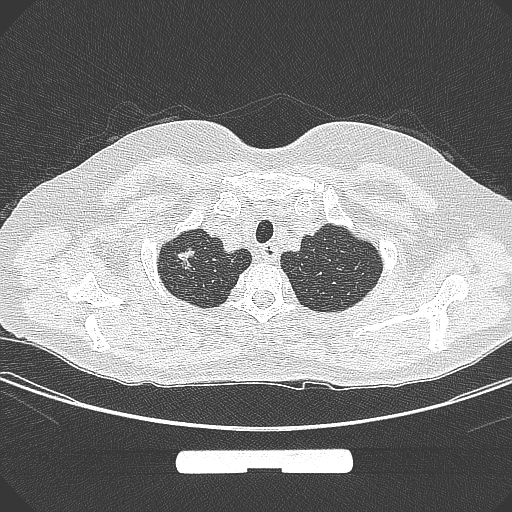
Chest CT, one axial slice; slice 263 of 295 in the series (ordered by position); 120 kVp; lung window (W 1500 / L -600 HU); 1 mm slice thickness; 512 × 512 image matrix, field of view 369 × 369 mm. Female patient, age 58 years. Case-level facts recorded for this patient, not image findings: clinical TNM (as recorded): T1b N0 M0.
Structures marked on this image (bounding box drawn by a radiologist):
- lung tumour (recorded histology: adenocarcinoma): bounding box [x1, y1, x2, y2] px = [174, 242, 202, 277]